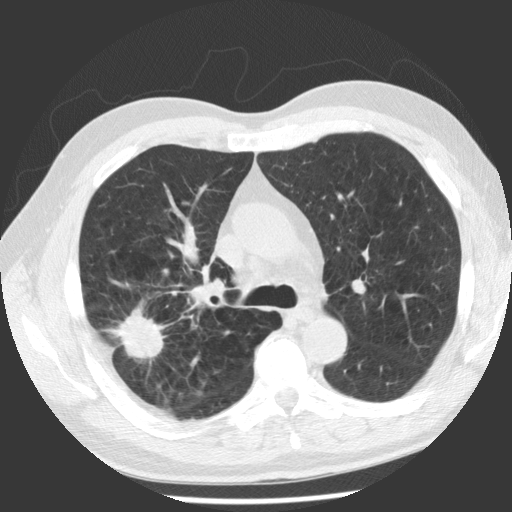
Low-dose screening chest CT, axial slice. First (baseline) screen. Lung window (W 1500 / L -600 HU). 2.5 mm slice thickness. Slice 74 of 112 in the series. Male, age 62 years at enrolment. Former smoker at enrolment.
- Expert reader's lesion annotation, bounding box <105,299,178,368> (left, top, right, bottom; pixels).
- The screening reader recorded 2 non-calcified nodules or masses ≥4 mm on this exam; which of them this box marks is not recorded.
- Official screen result: positive, change unspecified: nodule(s) >= 4 mm or enlarging nodule(s), mass(es), or other non-specific abnormalities suspicious for lung cancer.
- Lung cancer was diagnosed 71 days after this screen: adenocarcinoma, NOS, right upper lobe, poorly differentiated (G3), stage IV (AJCC 6th edition), 30 mm at pathology.